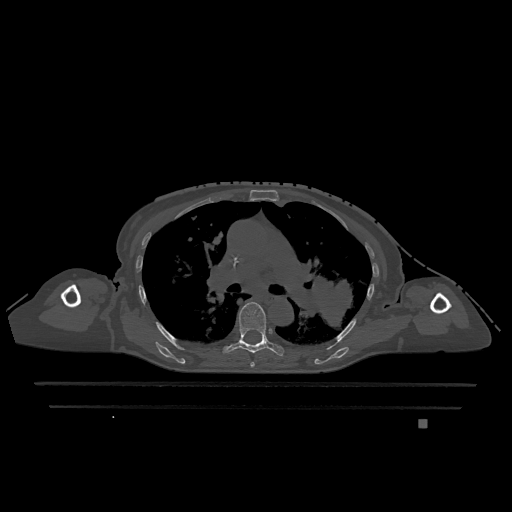
CT including the spine, one axial slice; position 792 of 1317 along the scan axis; bone window (W 1800 / L 400 HU); 0.5 mm slice thickness; 512 × 512 image matrix. Female patient, age 74 years. From the clinical record (not read from this slice): primary cancer: lung.
Outlined on this slice (semi-automatic segmentation, software-assisted and operator-edited):
- T5 vertebra: bounding box <250,362,255,368> (left, top, right, bottom; pixels)
- T6 vertebra: <223,302,284,356>